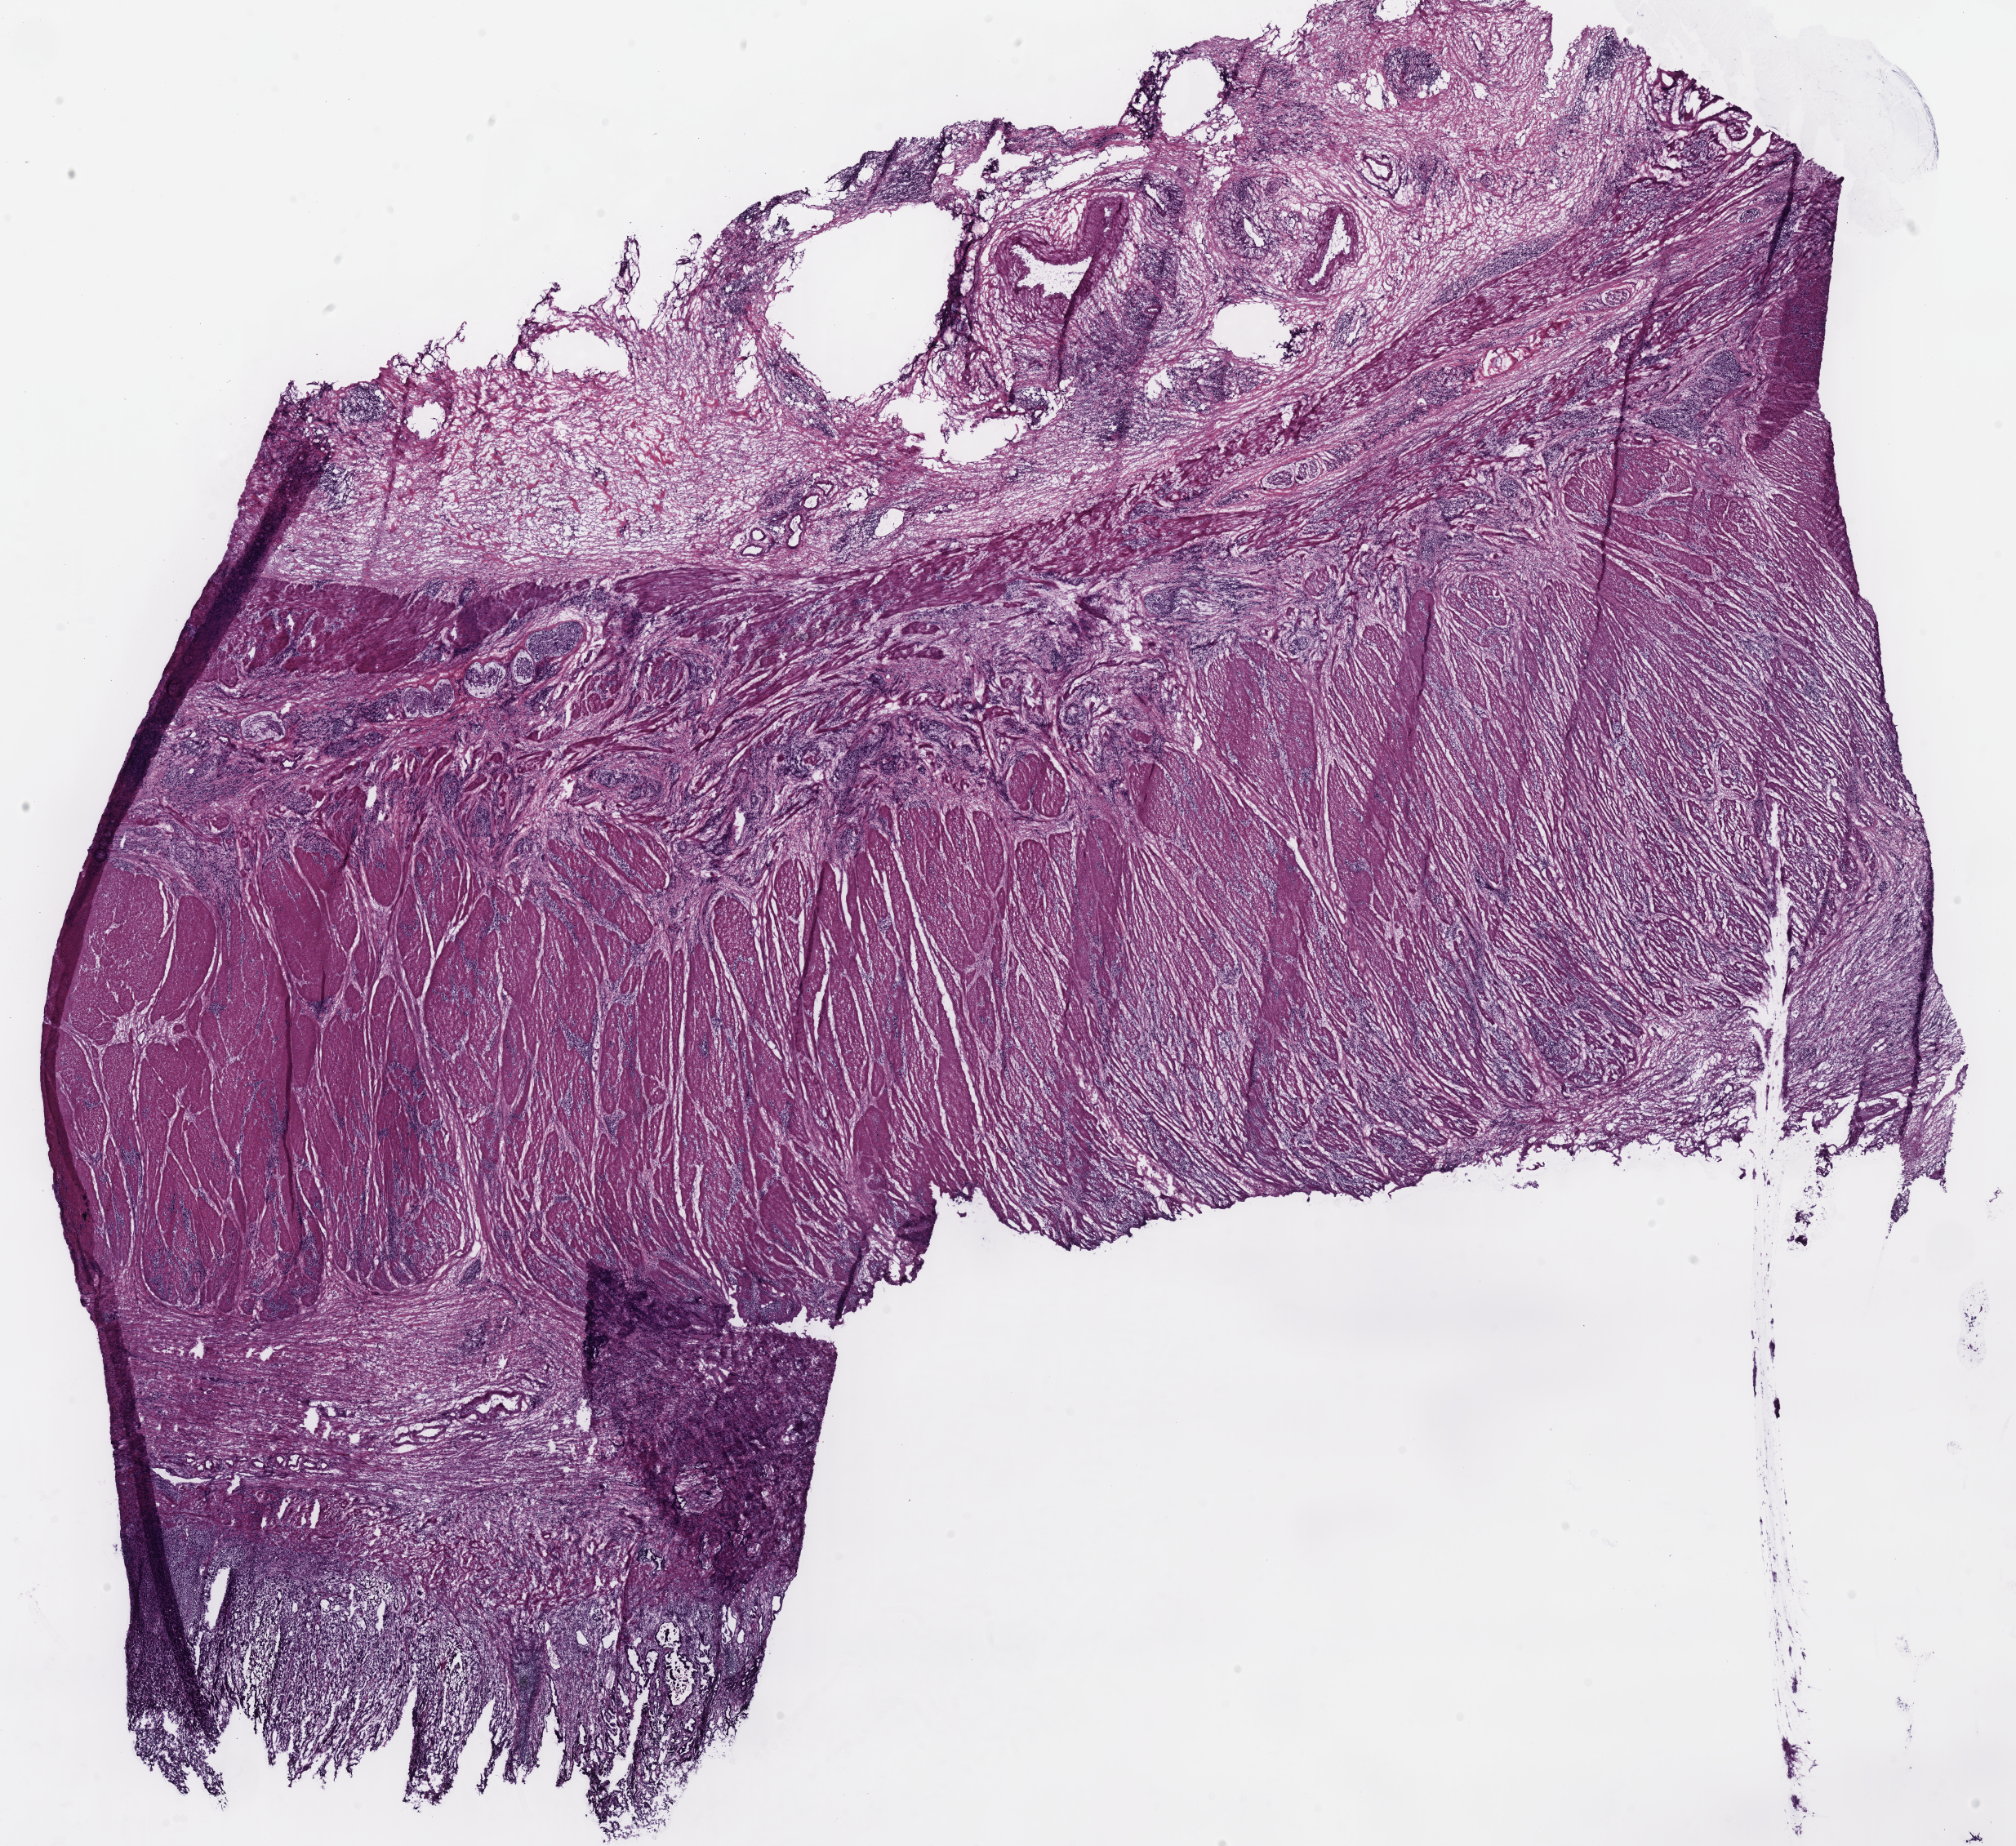
Whole-slide histology image, H&E — whole scanned area (about 19.5 x 17.8 mm, from a 40x scan) shown as a low-resolution overview; frozen section; sample: primary tumour, stomach. Male, age 58 years at initial diagnosis. Histologic grade: GX (grade cannot be assessed). Pathologist review of this section (percent, as recorded): tumour cells 30%, tumour nuclei 60%, normal cells 0%, stromal cells 70%, necrosis 0%.
Lymph nodes positive (case pathology): 11 of 11 examined. AJCC pathologic stage: IIIC (7th edition). Histologic diagnosis: Carcinoma, diffuse type (body of stomach).